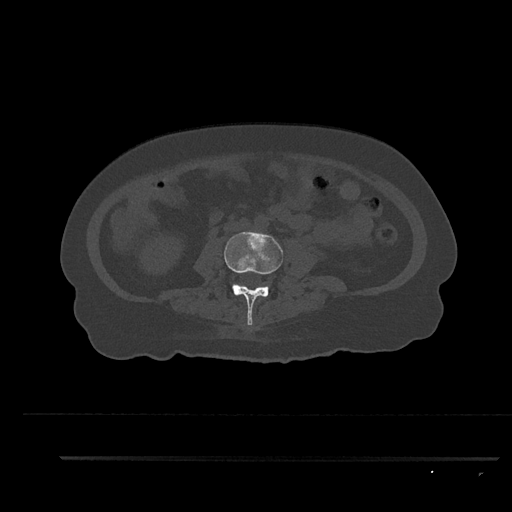
CT including the spine, one axial slice. Position 74 of 797 along the scan axis. Bone window (W 1800 / L 400 HU). 512 × 512 image matrix, field of view 408 × 408 mm. Patient: female, 44 years. From the clinical record (not read from this slice): primary cancer: renal.
Outlined on this slice (semi-automatic segmentation, software-assisted and operator-edited):
- L3 vertebra: bounding box [x1, y1, x2, y2] px = [224, 231, 283, 326]